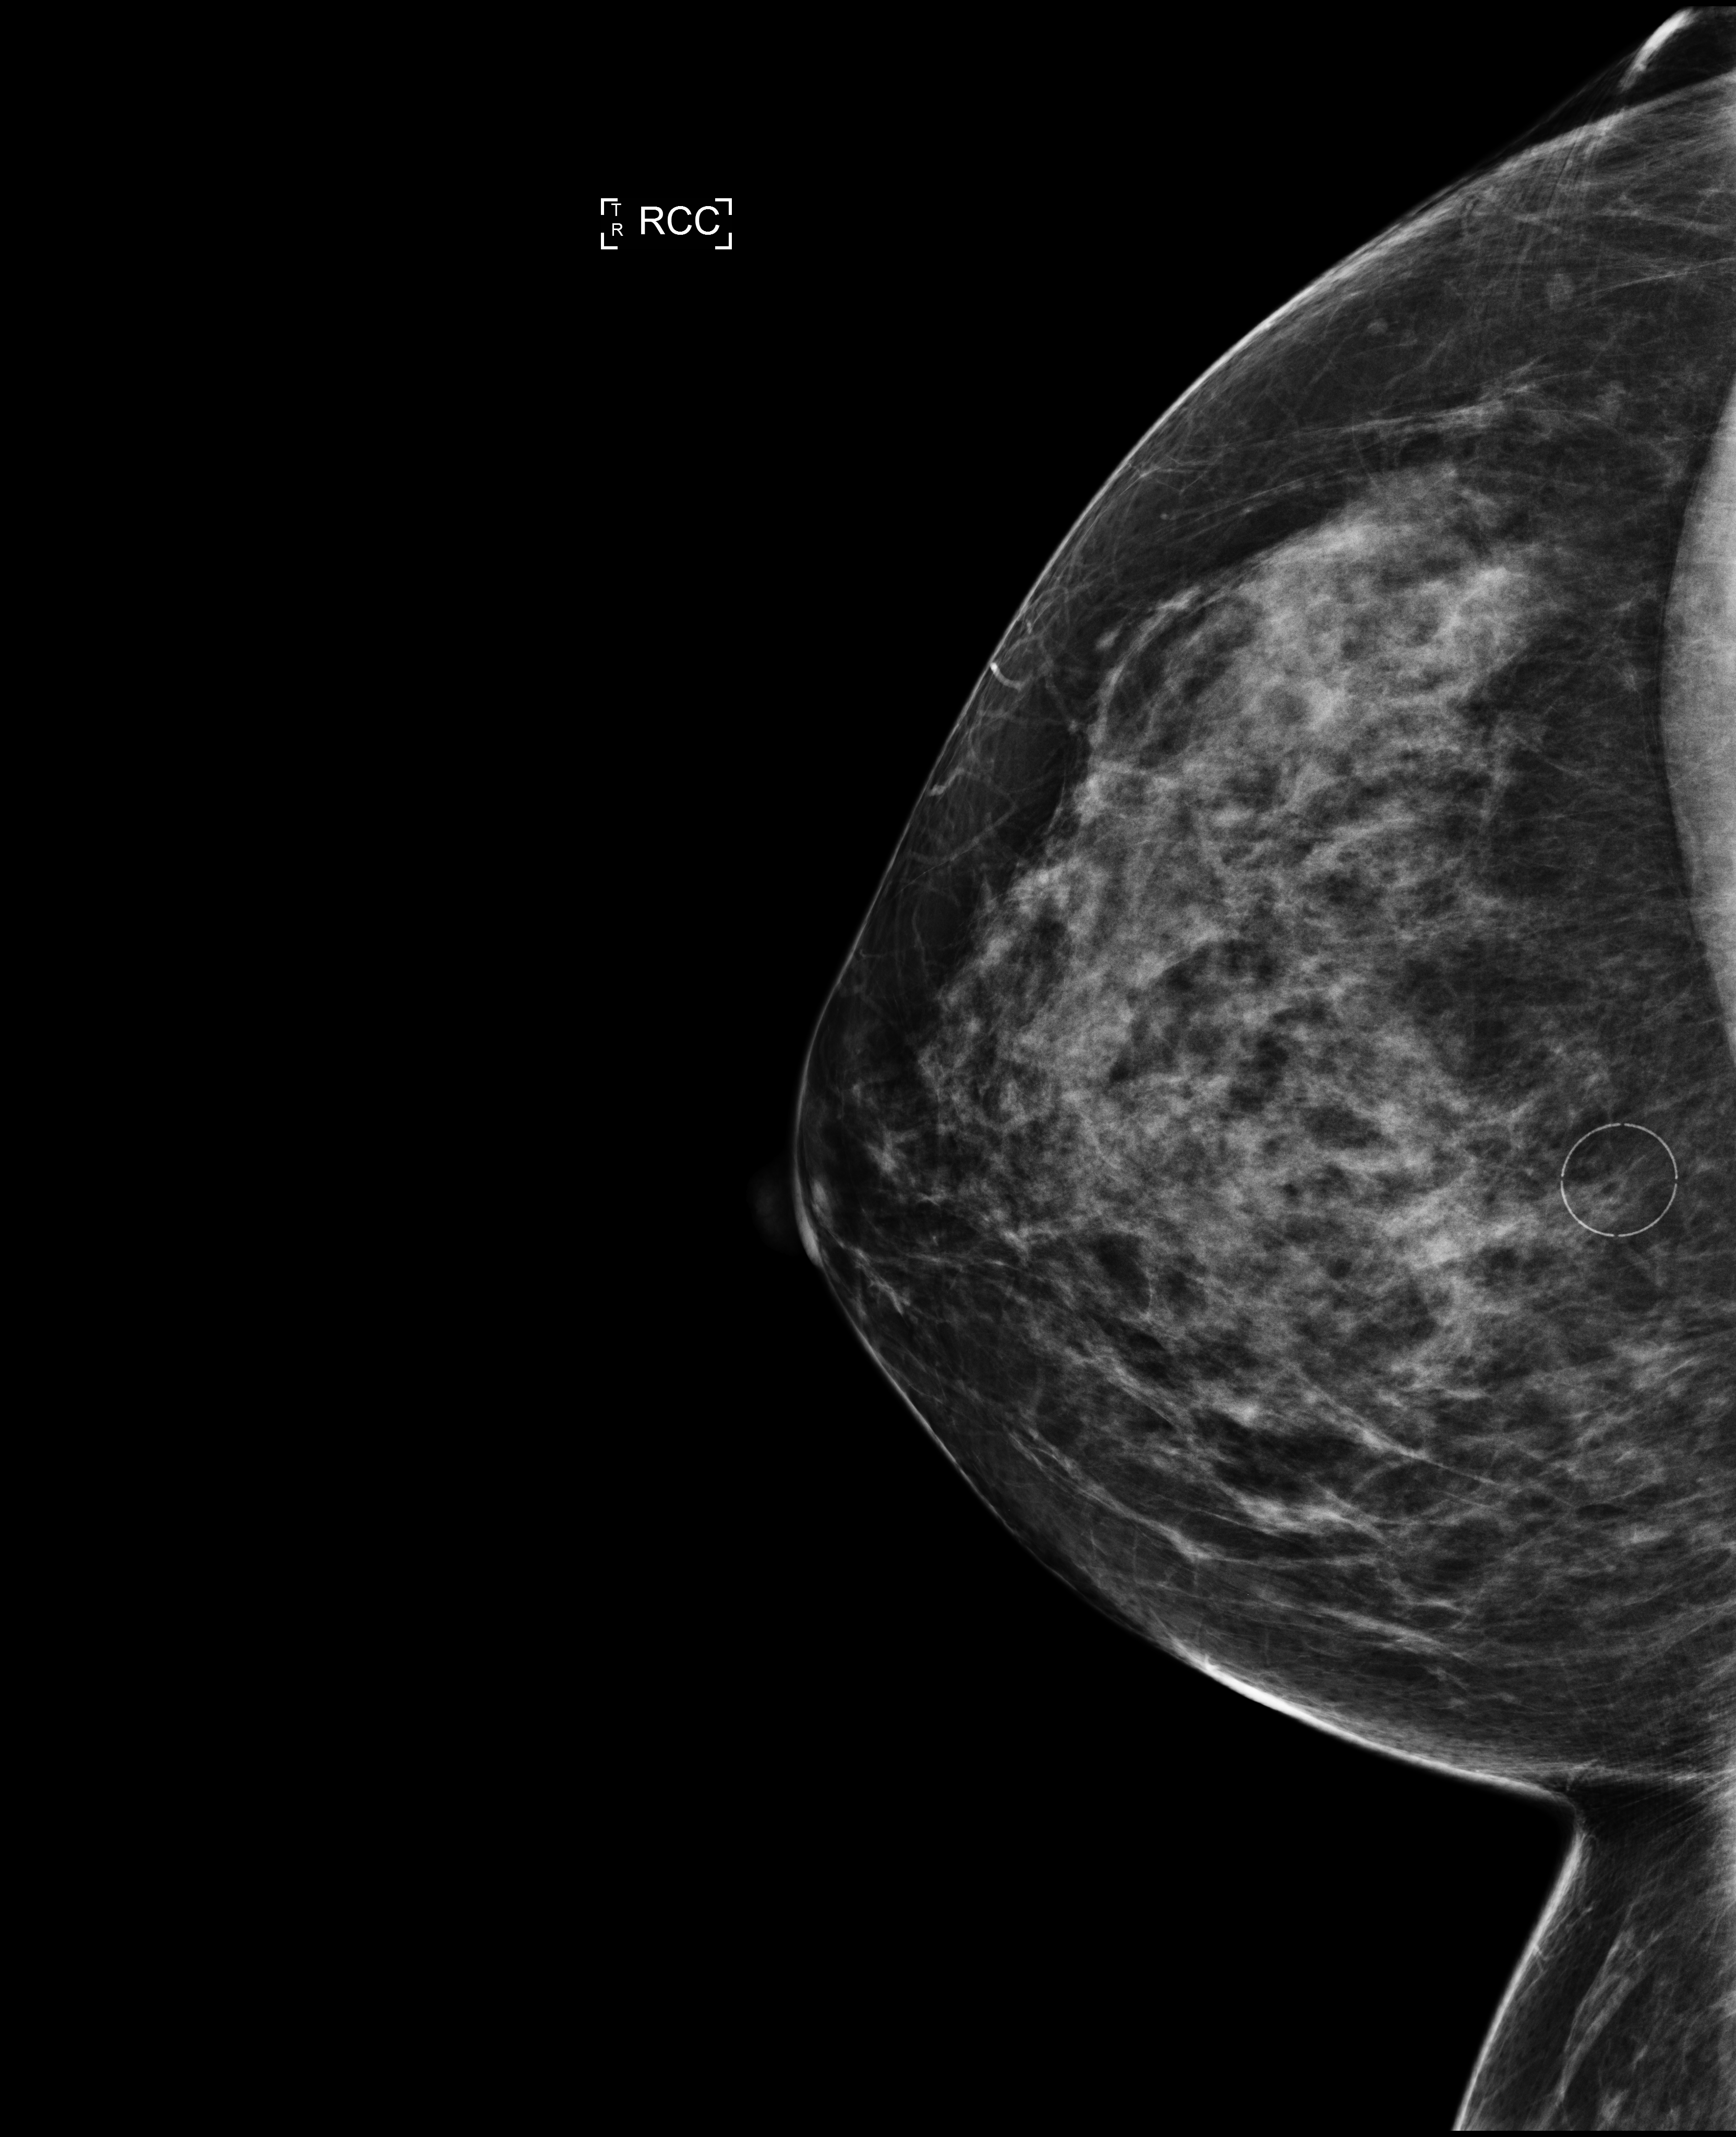
Full-field digital mammogram (FFDM), right breast, cranio-caudal projection, screening examination, compressed breast thickness 81 mm. Patient aged 46 years (female).
BI-RADS breast density category at the screening exam (both breasts, scale 1–4): 3. Final BI-RADS assessment for this screening round (tomosynthesis exam, both breasts): category 1. Recall: no recall after this screen.